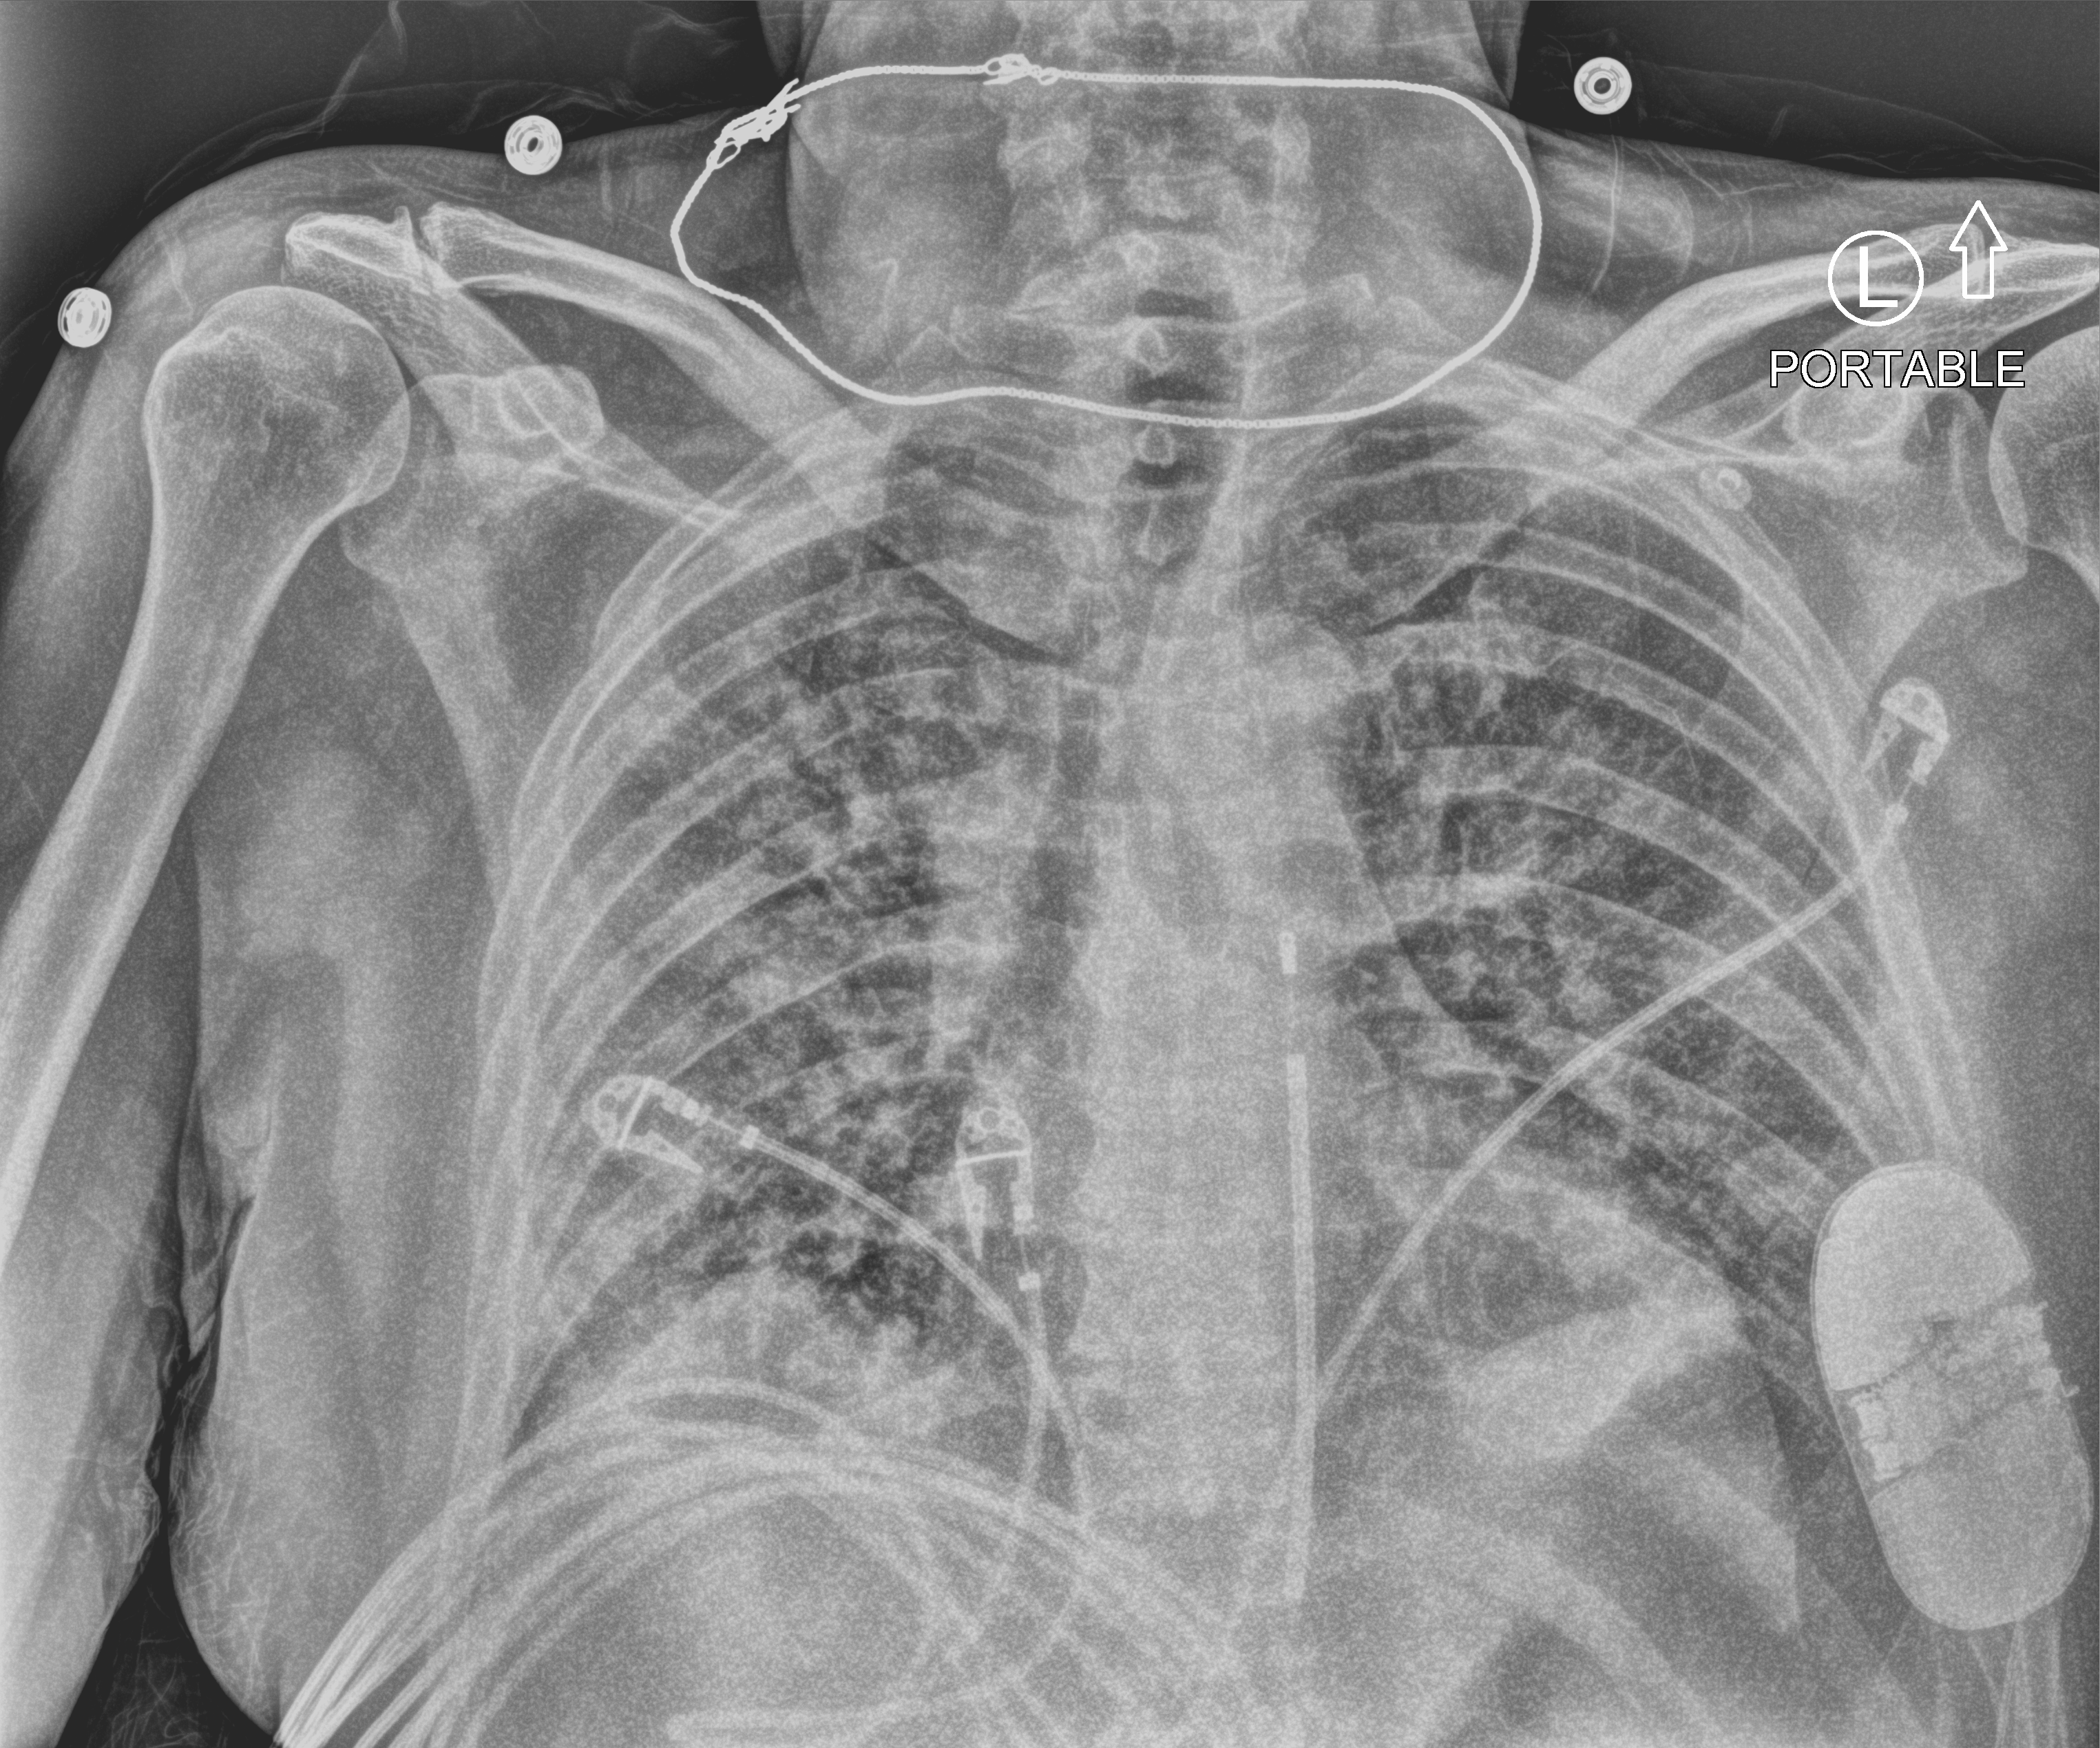
Bedside chest radiograph (computed radiography); anteroposterior (AP) projection. Patient hospitalised with COVID-19; male, aged 18–59 years.
Hospital-stay facts (about this admission, not read from this image; timing relative to this image not recorded):
- admitted to intensive care during this hospital stay: no
- mechanically ventilated during this hospital stay: no
- COPD (admission record): no